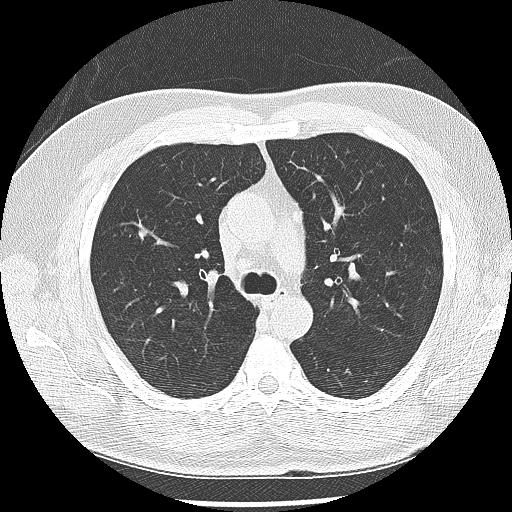
Low-dose screening chest CT, one axial slice. Position 179 of 265 along the scan axis. Reconstruction kernel LUNG. 120 kVp. Lung window (W 1500 / L -600 HU). 512 × 512 image matrix.
Annotated regions visible in this slice (expert manual segmentation):
- lesion 1 (tumor, upper lobe of right lung): bounding box [x1, y1, x2, y2] px = [139, 227, 150, 241]